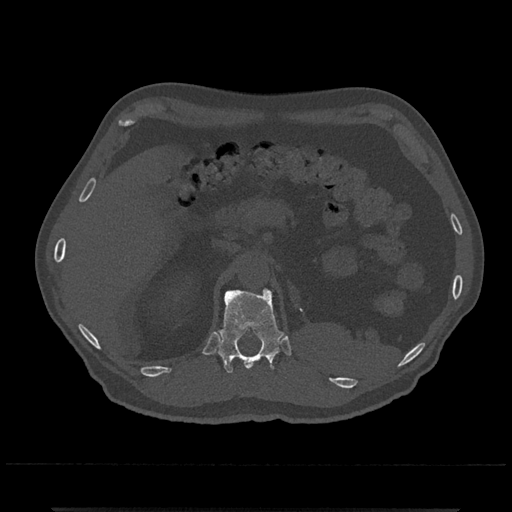
CT including the spine, one axial slice; position 437 of 797 along the scan axis; 120 kVp; bone window (W 1800 / L 400 HU); 0.5 mm slice thickness; 512 × 512 image matrix. Male patient, age 67 years. Case-level facts recorded for this patient, not image findings: primary cancer: prostate.
Structures marked on this image (semi-automatic segmentation, software-assisted and operator-edited):
- T12 vertebra: box from (x=217, y=288) to (x=283, y=373) px